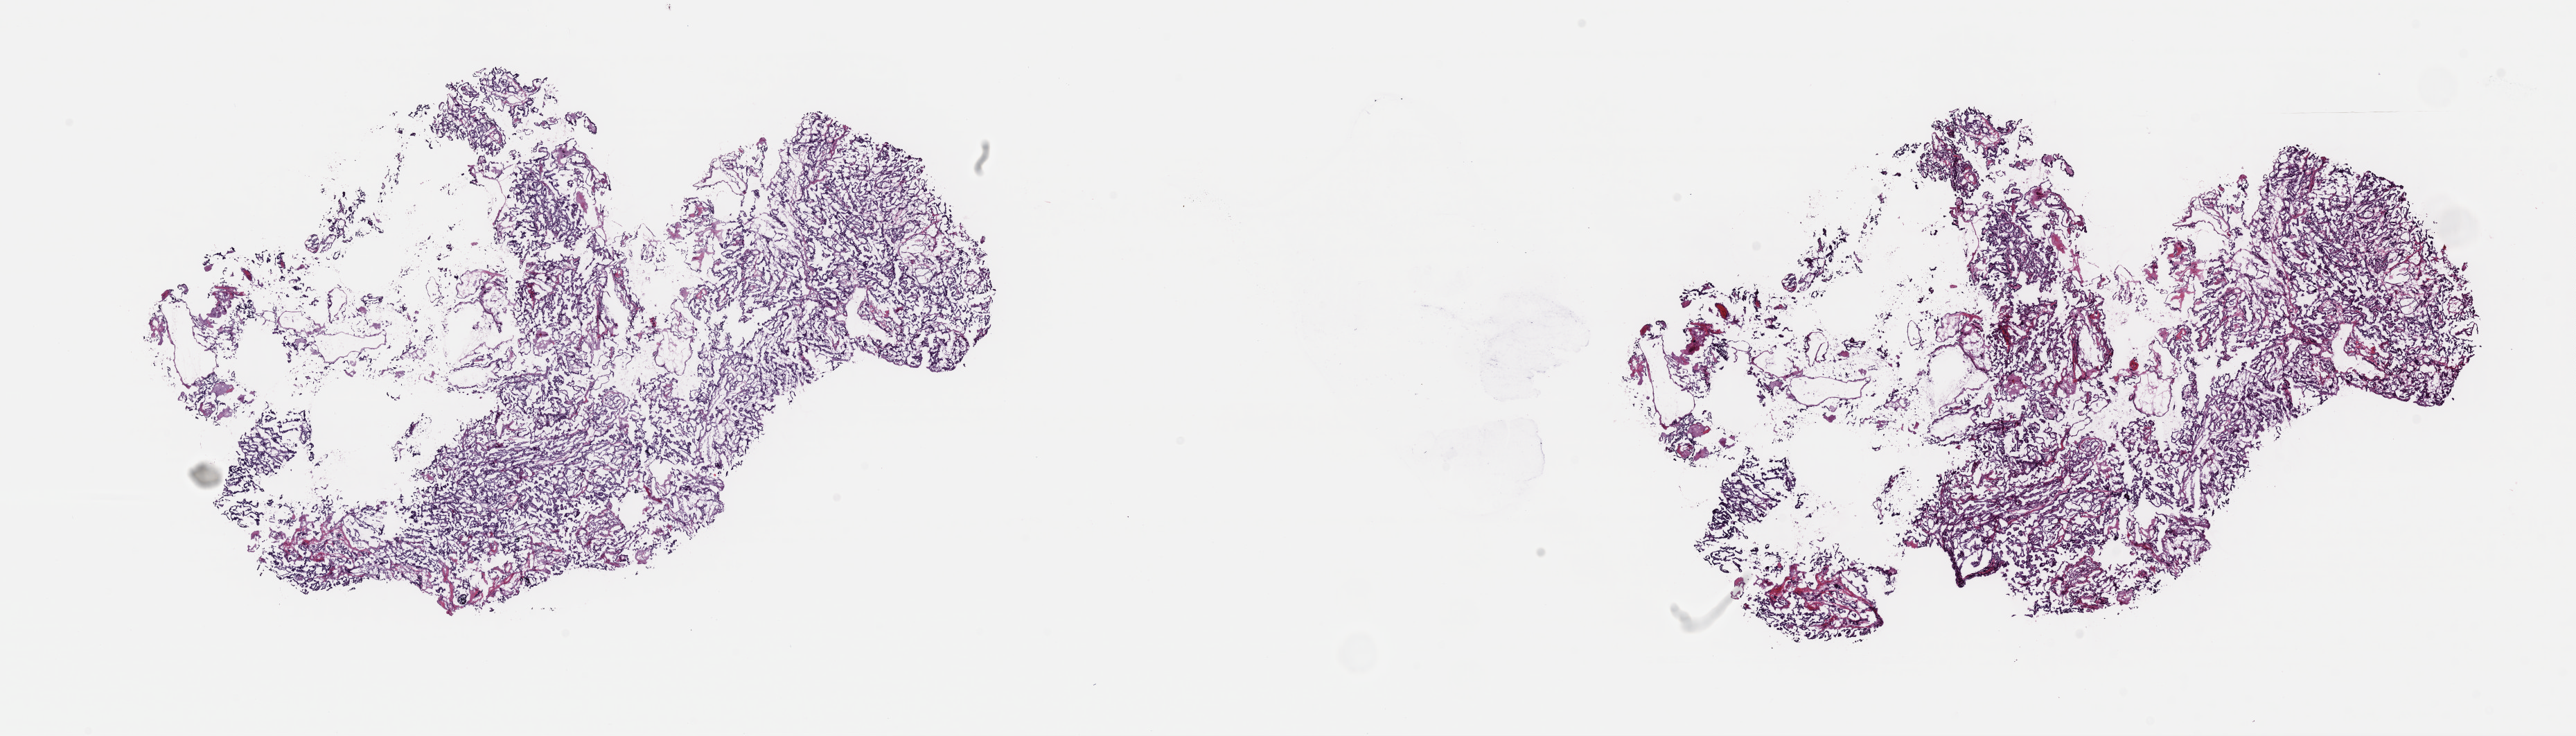
Whole-slide histology image, Hematoxylin and eosin (H&E) stained — whole scanned area (about 29.4 x 8.4 mm, from a 40x scan) shown as a low-resolution overview, frozen section, primary tumour sample from the thyroid. Patient: male, age at initial diagnosis 65 years.
Histologic diagnosis: Papillary adenocarcinoma, NOS (thyroid gland).